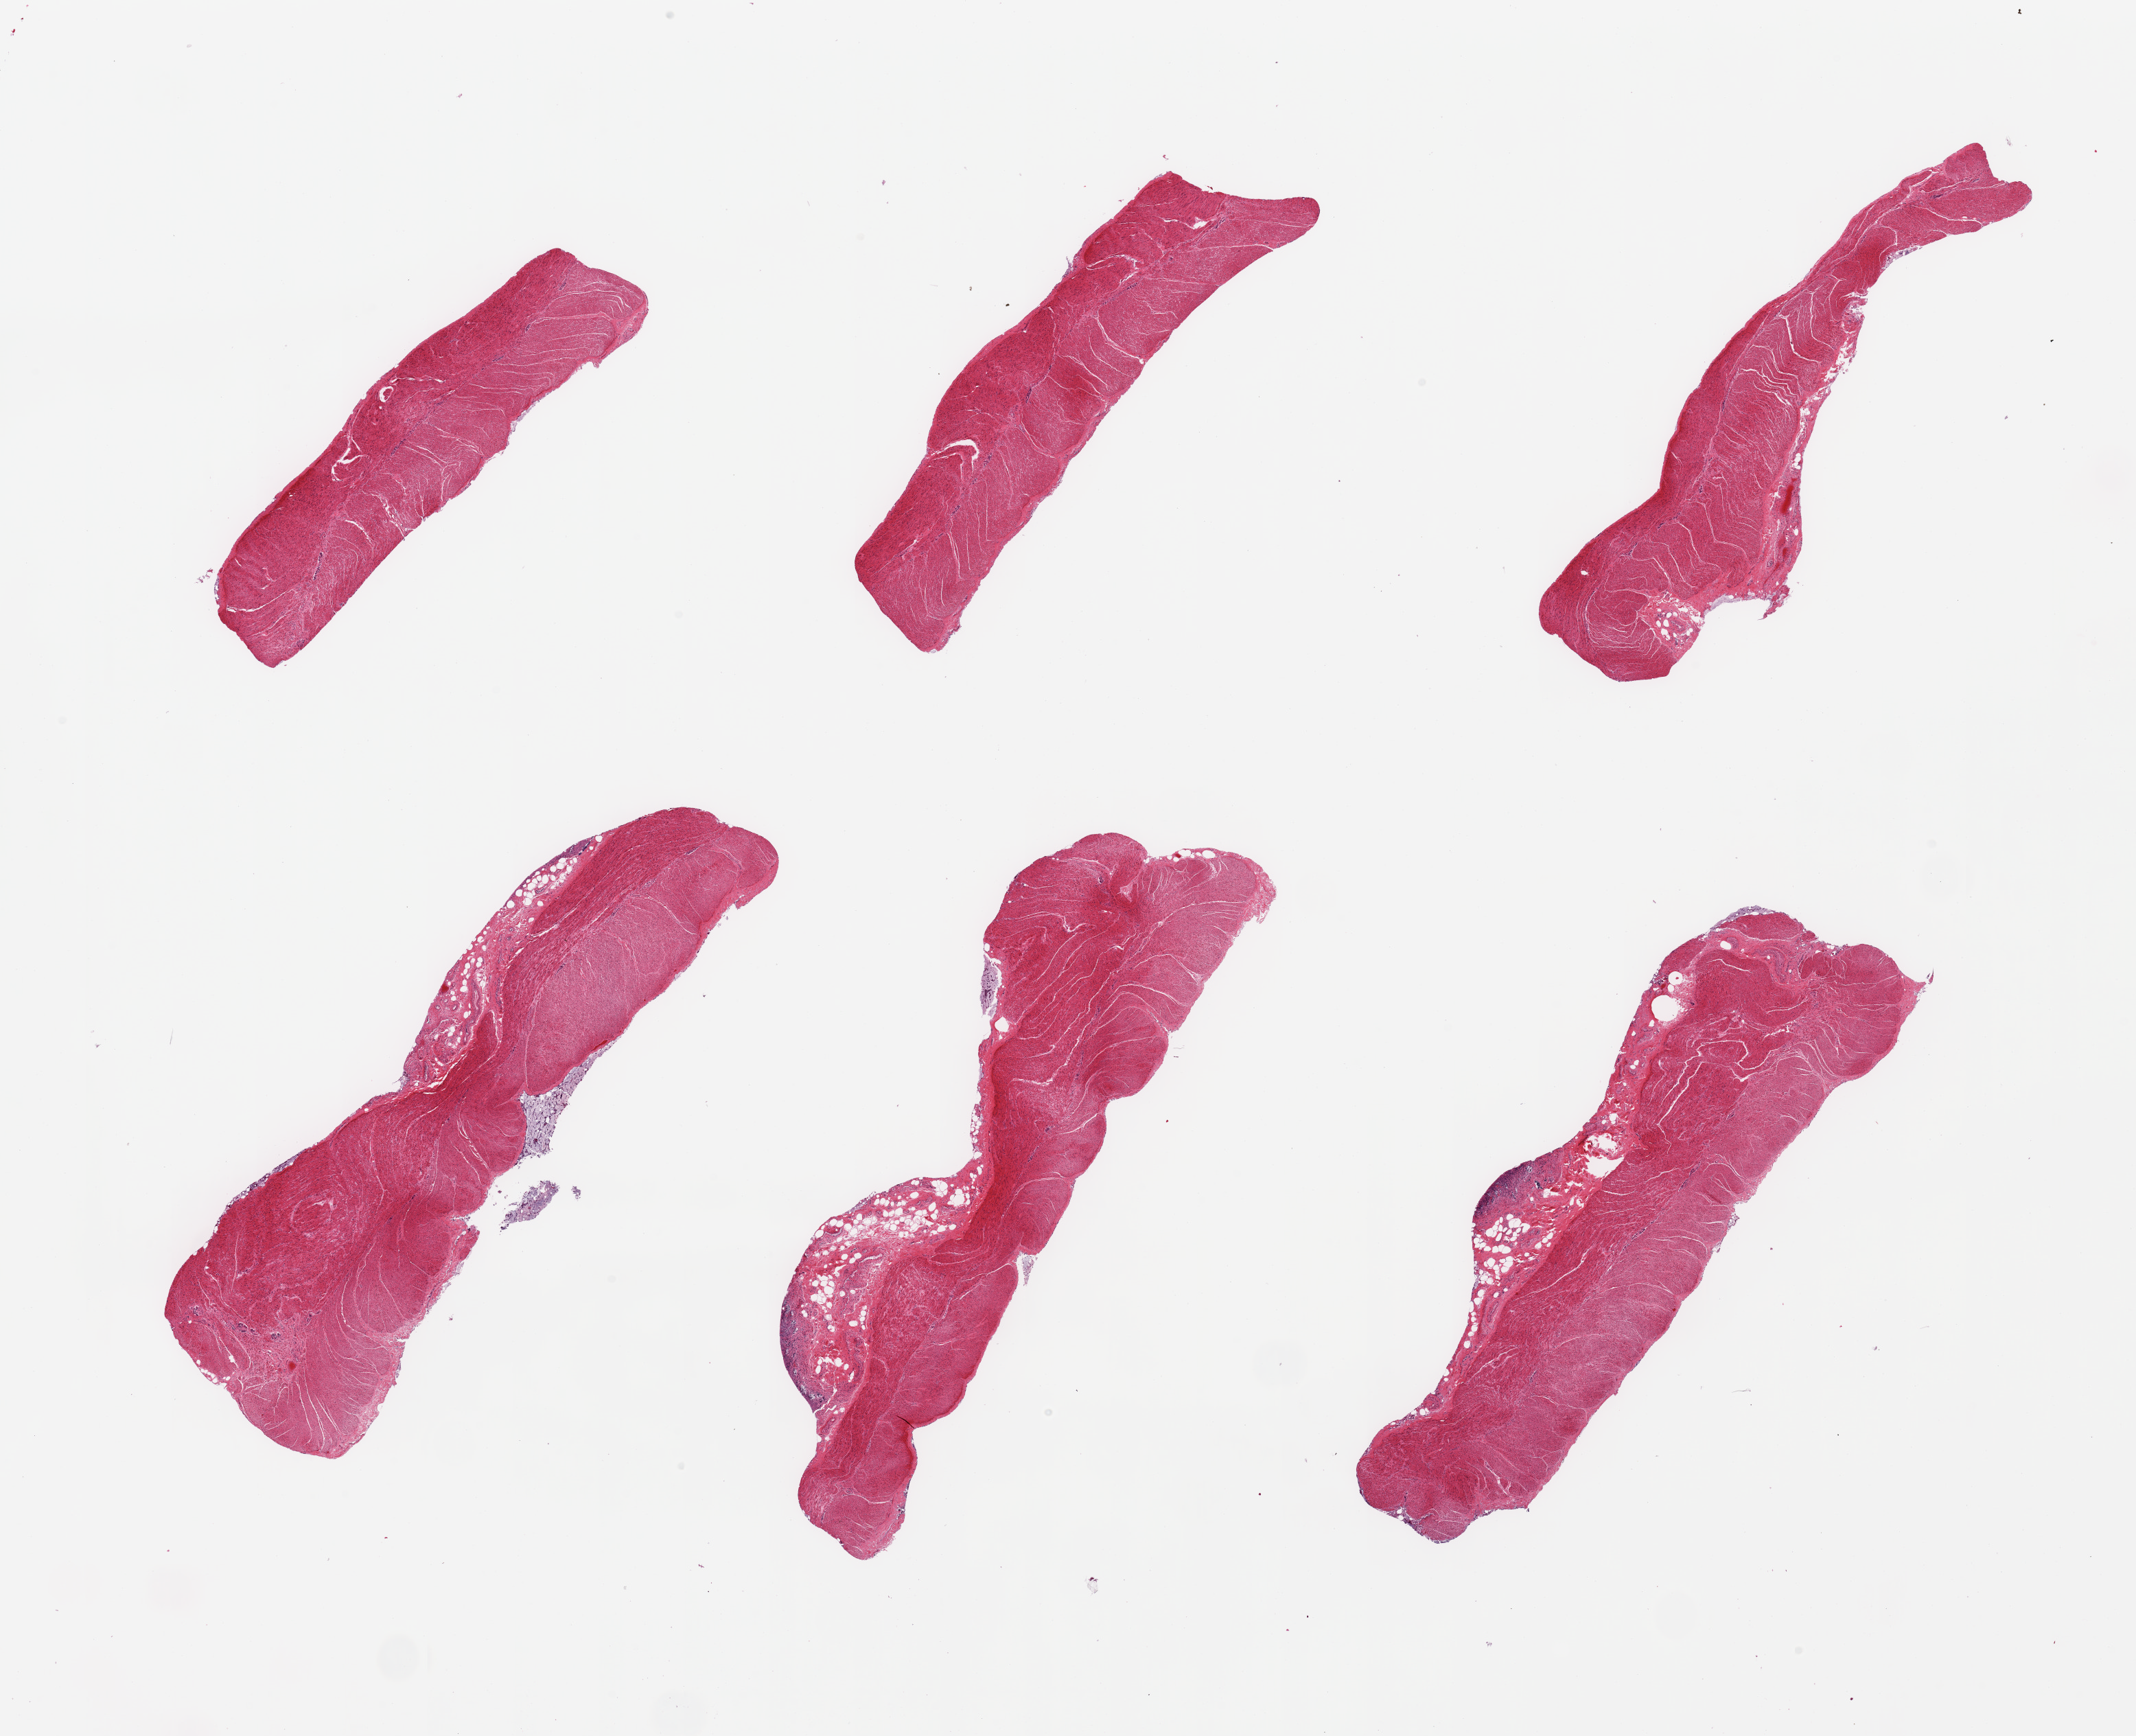
Hematoxylin and eosin (H&E) whole-slide image — whole scanned area (about 24.6 x 20.0 mm, acquisition: 20x scan) shown as a low-resolution overview, PAXgene-fixed, paraffin-embedded tissue, sampled site (target tissue): sigmoid colon, donor tissue sample. Male donor.
Reviewer comment on this tissue sample: 6 pieces, confirmed target muscularis, adherent serosa/fat up to 1mm nubbins.